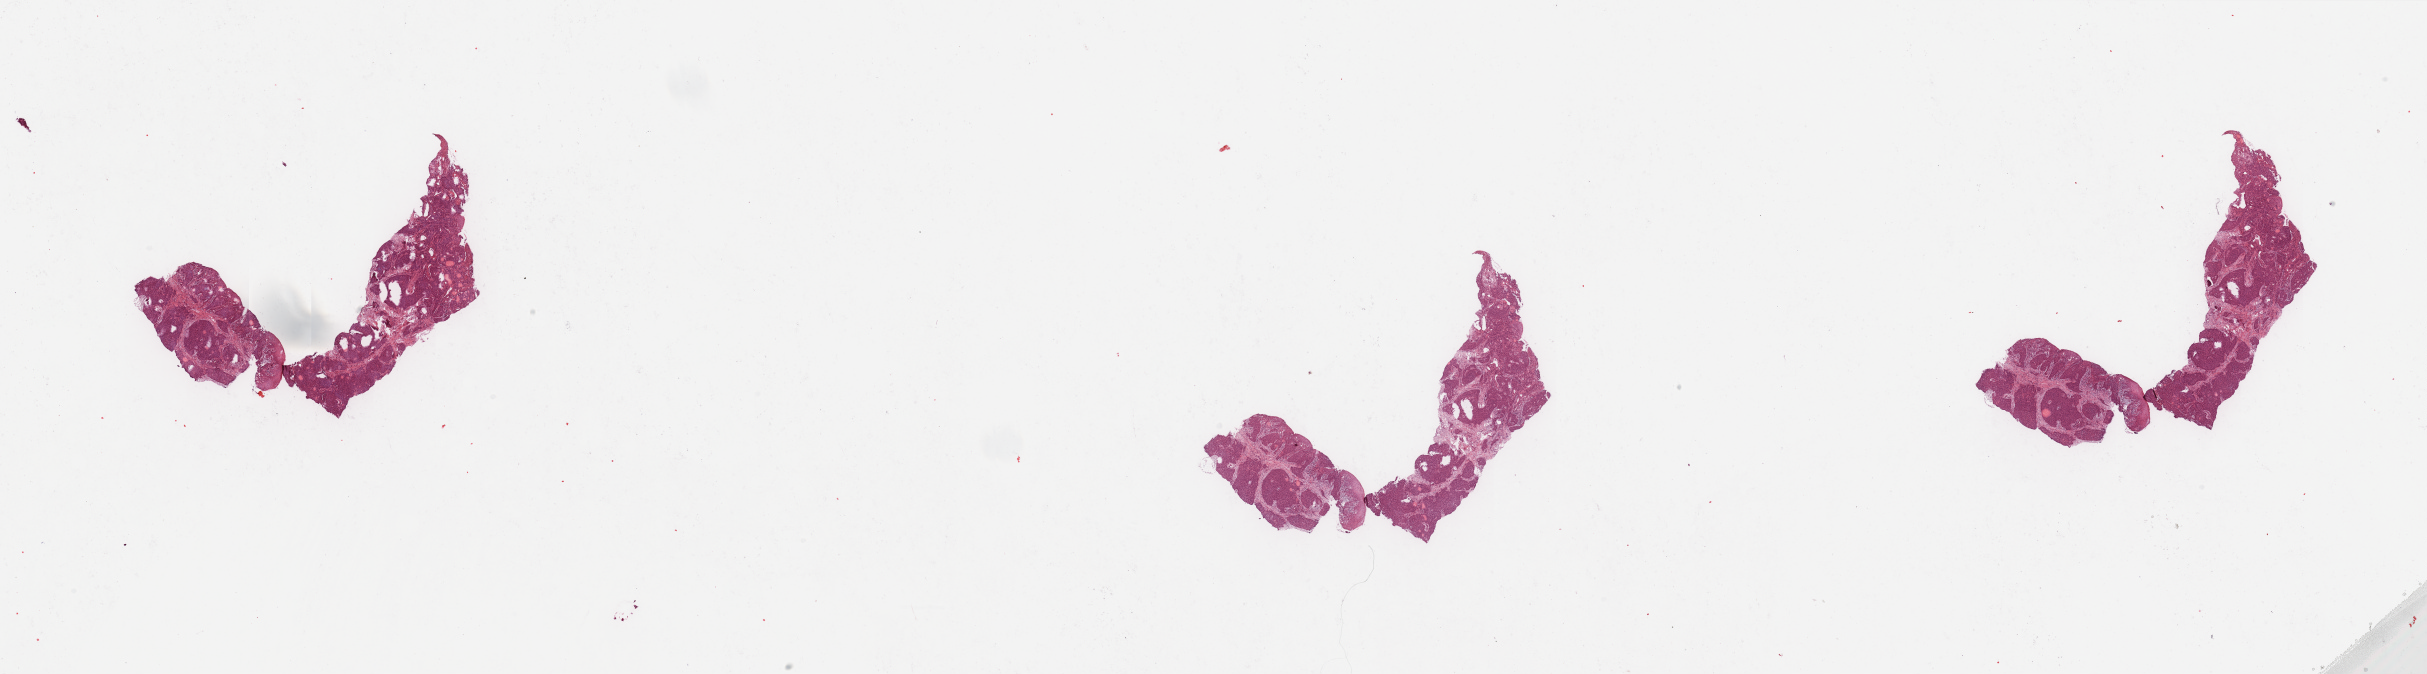
Digitized H&E tissue section (whole slide), a low-resolution overview of the entire scanned area, about 38.4 x 10.7 mm (acquisition: 20x scan), tumour tissue sample, sampled site: oropharynx. Male, 73 y/o. Histologic grade: G2 (moderately differentiated). Slide review estimates, as recorded: tumour nuclei 90%, necrosis 3%.
Histologic diagnosis: Squamous cell carcinoma, NOS. Primary tumour site (as recorded): oropharynx. AJCC pathologic stage: II.